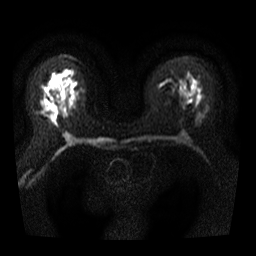
Breast MRI, one axial slice; position 20 of 40 along the scan axis; diffusion-weighted series; image 2 of 4 stored at this slice position (different b-values; order by instance number); 3 T; 5 mm slice thickness; 256 × 256 image matrix, field of view 300 × 300 mm. Female patient.
Structures marked on this image (outlined manually by an expert reader):
- tumour on diffusion-weighted imaging: box from (x=49, y=111) to (x=57, y=121) px